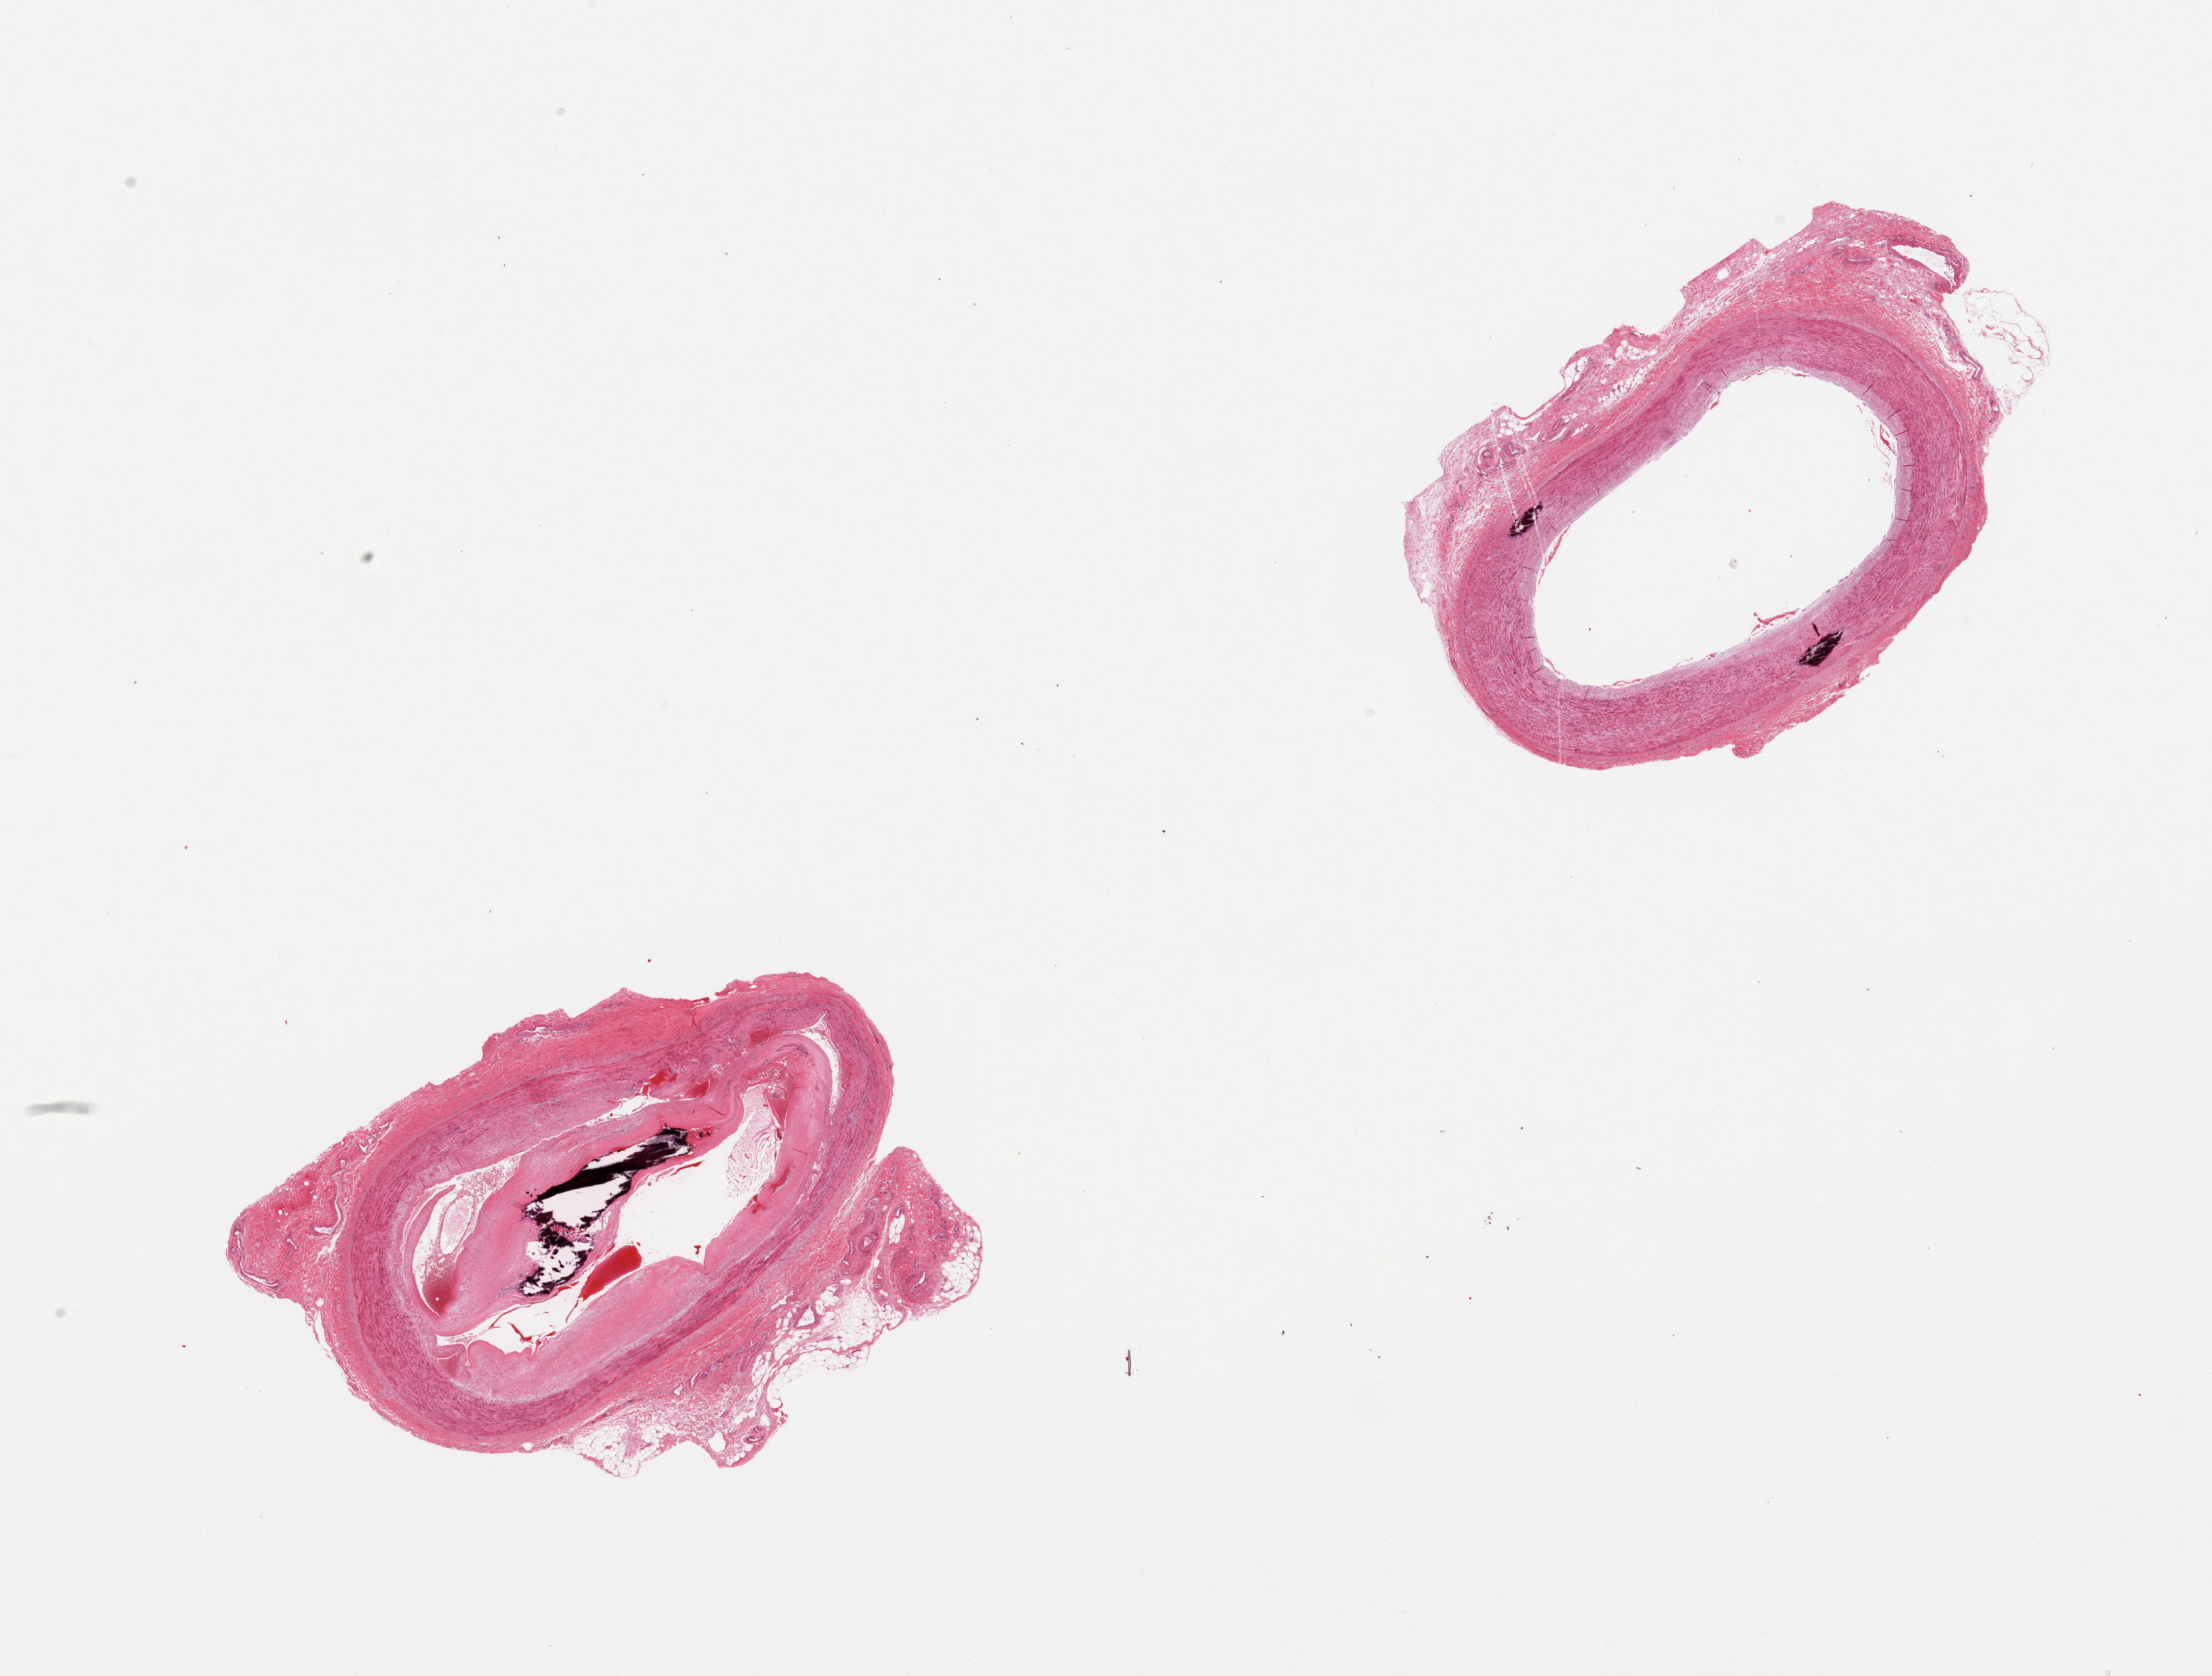
Whole-slide image, H&E stain, brightfield — low-resolution overview of the scanned area, about 24.6 x 18.6 mm (from a 20x scan); PAXgene-fixed paraffin-embedded (PFPE) section; target tissue: tibial artery; tissue donor sample. Male donor.
Review note (as recorded): 2 pieces, one piece demonstrates calcific atherosclerosis with narrowing of the lumen, second piece has focal medial calcification (Monckeberg's sclerosis).